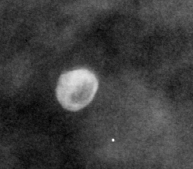
Region of interest cut from a scanned film mammogram (one marked finding), right breast, CC view, BI-RADS breast density category 3 (scale 1–4).
Finding: calcifications, morphology round and regular / eggshell; BI-RADS assessment category 2; benign without callback (not worked up further).